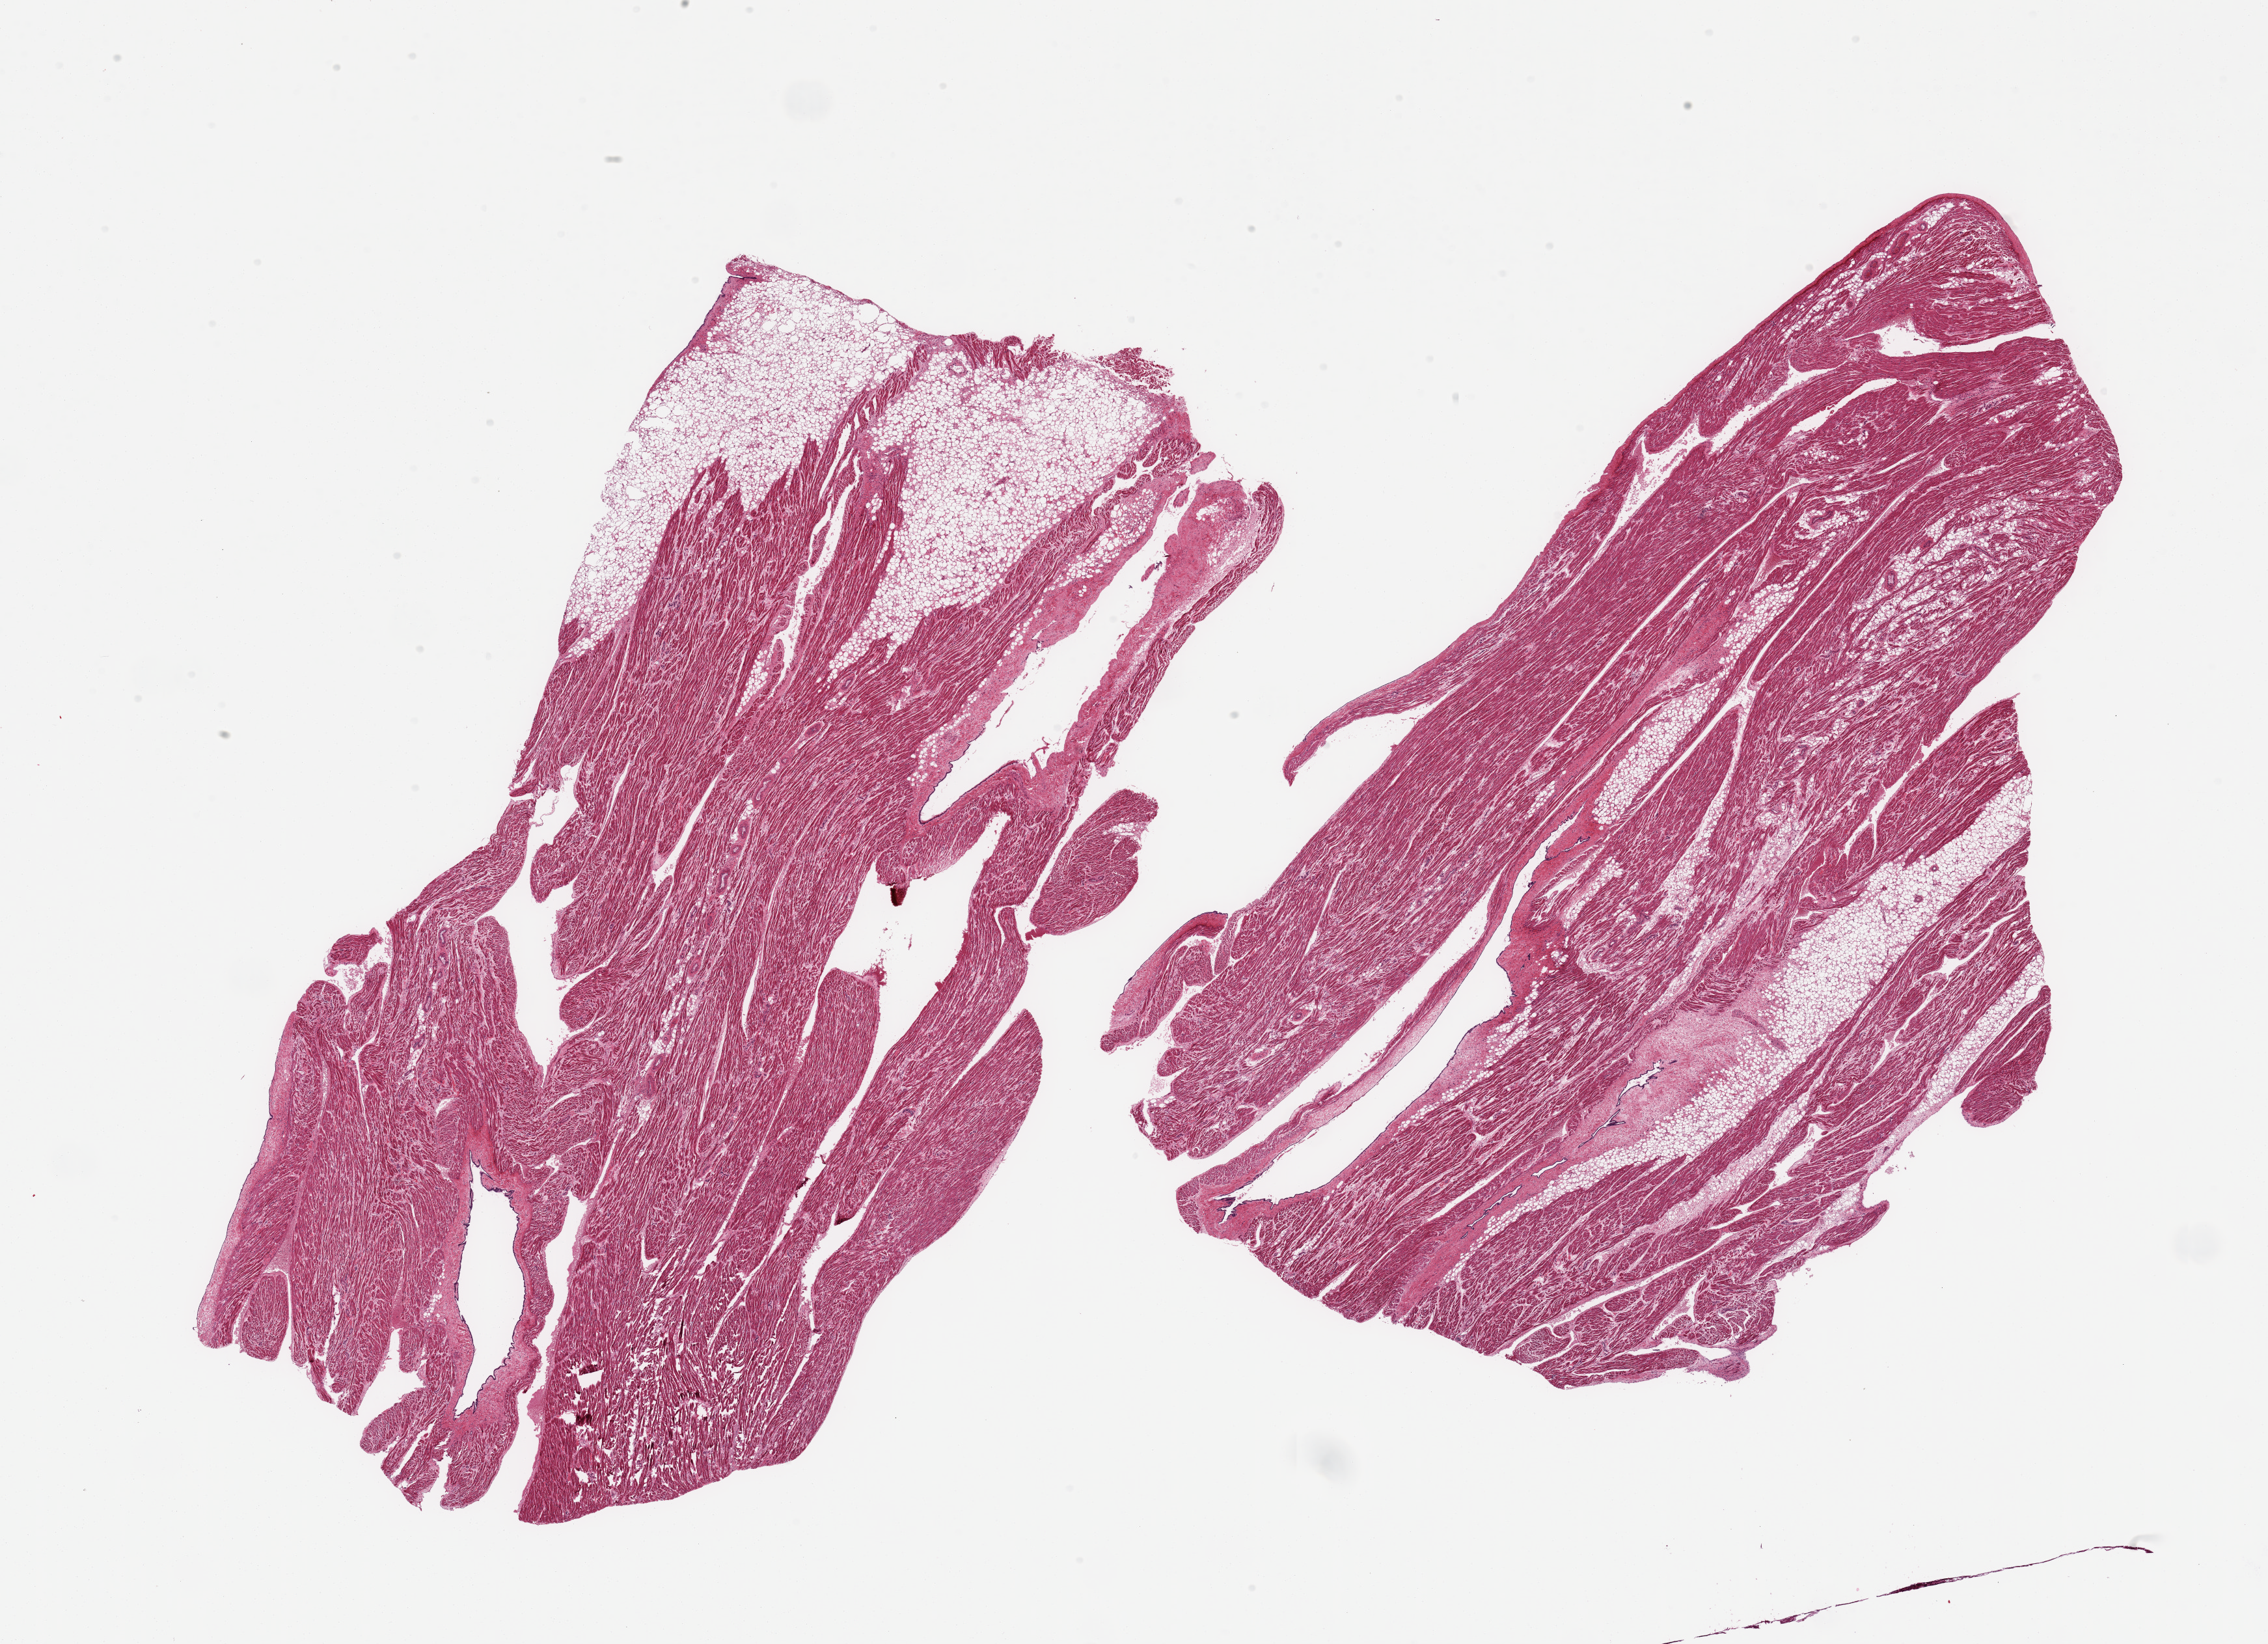
Whole-slide image, H&E stain, low-resolution overview of the scanned area, about 27.6 x 20.0 mm (slide scanned at 20x); PAXgene-fixed paraffin-embedded (PFPE) section; sampled site (target tissue): auricular appendage; tissue donor sample.
Reviewer comment on this tissue sample: 2 pieces; ~20% internal fat.